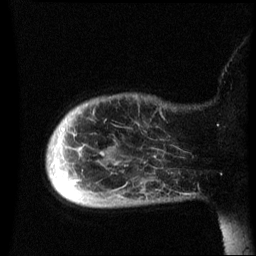
Breast MRI (dynamic contrast-enhanced), one sagittal slice; position 8 of 60 along the scan axis; dynamic contrast-enhanced series, image 2 of 3 at this slice position (ordered by acquisition); 1.5 T; TE 4.2 ms, TR 8.4 ms; 256 × 256 image matrix. Patient: female, 49 years.
Outlined on this slice (semi-automatic segmentation, software-assisted and operator-edited):
- analysis volume of interest (the breast-tissue region the enhancement analysis was run in; not a lesion): bounding box (x1, y1, x2, y2) in pixels: (47, 94, 184, 209)
- tumour enhancement mask (voxels above the 70 % enhancement threshold inside the analysis volume of interest): (103, 154, 105, 157)